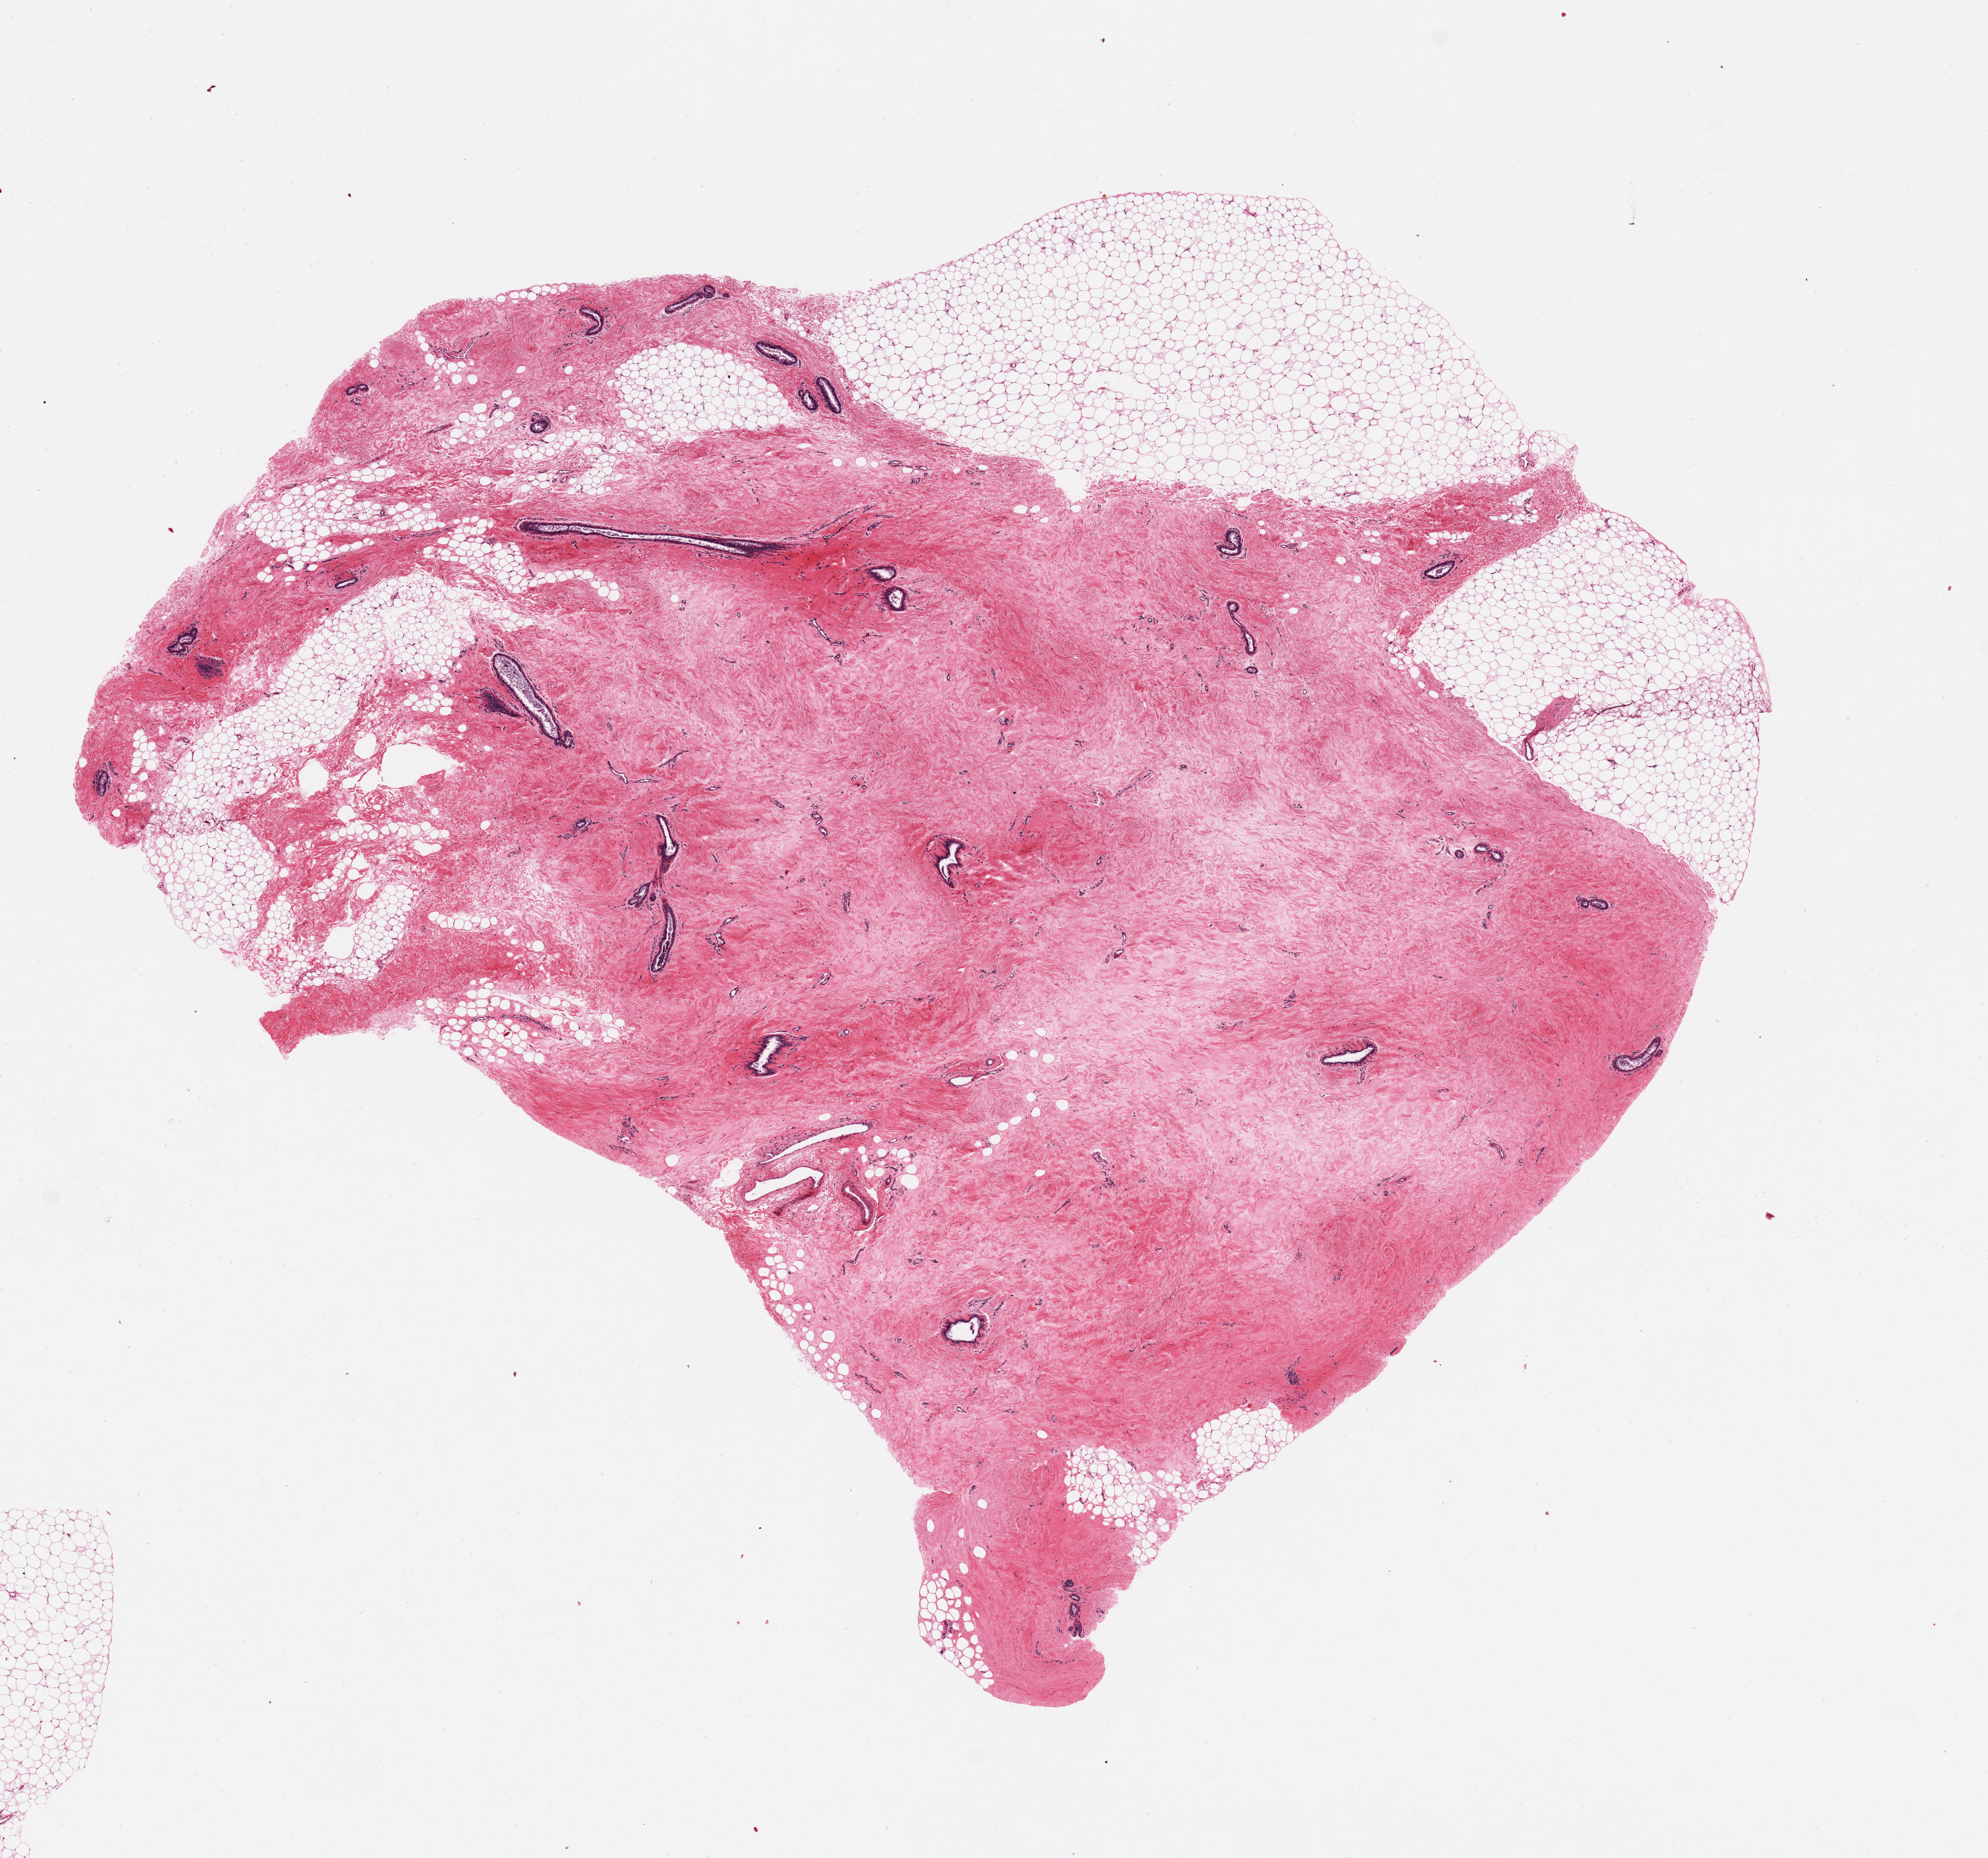
Digitized H&E-stained section — shown as a low-resolution overview of the whole scanned area (about 11.8 x 11.0 mm), PAXgene-fixed, paraffin-embedded tissue, section of breast (target tissue), tissue donor sample. Donor: male.
Pathologist's review note for this sample: 1 piece, gynecomastoid stromal hyperplasia; duct elements.